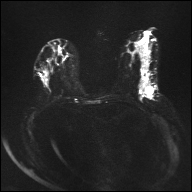
Breast MRI, one axial slice; diffusion-weighted series; image 2 of 4 stored at this slice position (different b-values; order by instance number); 1.5 T; 4 mm slice thickness; 192 × 192 image matrix, field of view 360 × 360 mm. Female patient.
Outlined on this slice (outlined manually by an expert reader):
- tumour on diffusion-weighted imaging: bounding box <141,80,148,92> (left, top, right, bottom; pixels)